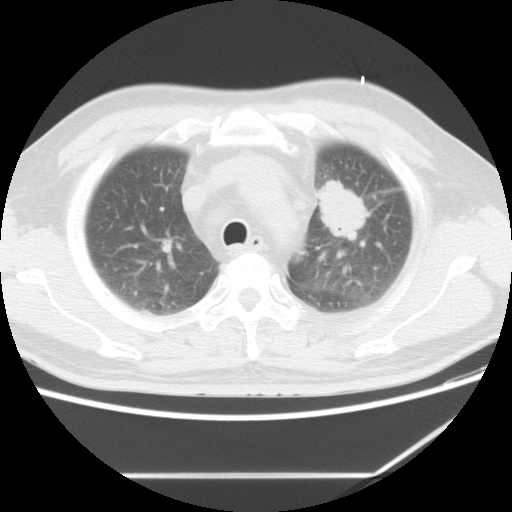
Chest CT, one axial slice. Reconstruction kernel STANDARD. 120 kVp. Lung window (W 1500 / L -600 HU). 512 × 512 image matrix. Male patient, age 56 years. Case-level facts recorded for this patient, not image findings: clinical TNM (as recorded): T2 N3 M1.
Structures marked on this image (rectangle marked by the reading radiologist):
- lung tumour (recorded histology: adenocarcinoma): box from (x=319, y=173) to (x=369, y=248) px